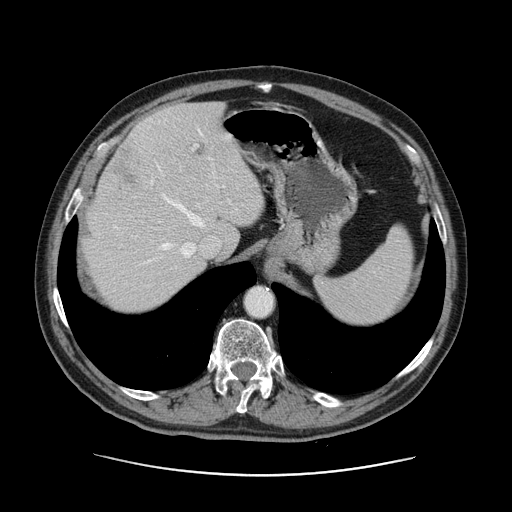
Contrast-enhanced abdominal CT, one axial slice. Position 99 of 141 along the scan axis. 120 kVp. Intravenous contrast given. Soft-tissue window (W 400 / L 40 HU). 512 × 512 image matrix, field of view 395 × 395 mm. Male patient, age 72 years. From the clinical record (not read from this slice): diagnosis: colorectal cancer liver metastases, imaged before liver resection; multiple liver metastases: yes; largest metastasis: 5.4 cm.
Outlined on this slice (outlined manually by an expert reader):
- hepatic veins: bounding box (x1, y1, x2, y2) in pixels: (145, 129, 211, 263)
- liver: (84, 102, 265, 315)
- planned liver remnant (the part of the liver to remain after resection): (88, 102, 264, 314)
- portal vein (with intrahepatic branches): (183, 145, 230, 254)
- liver metastasis: (110, 143, 136, 184)